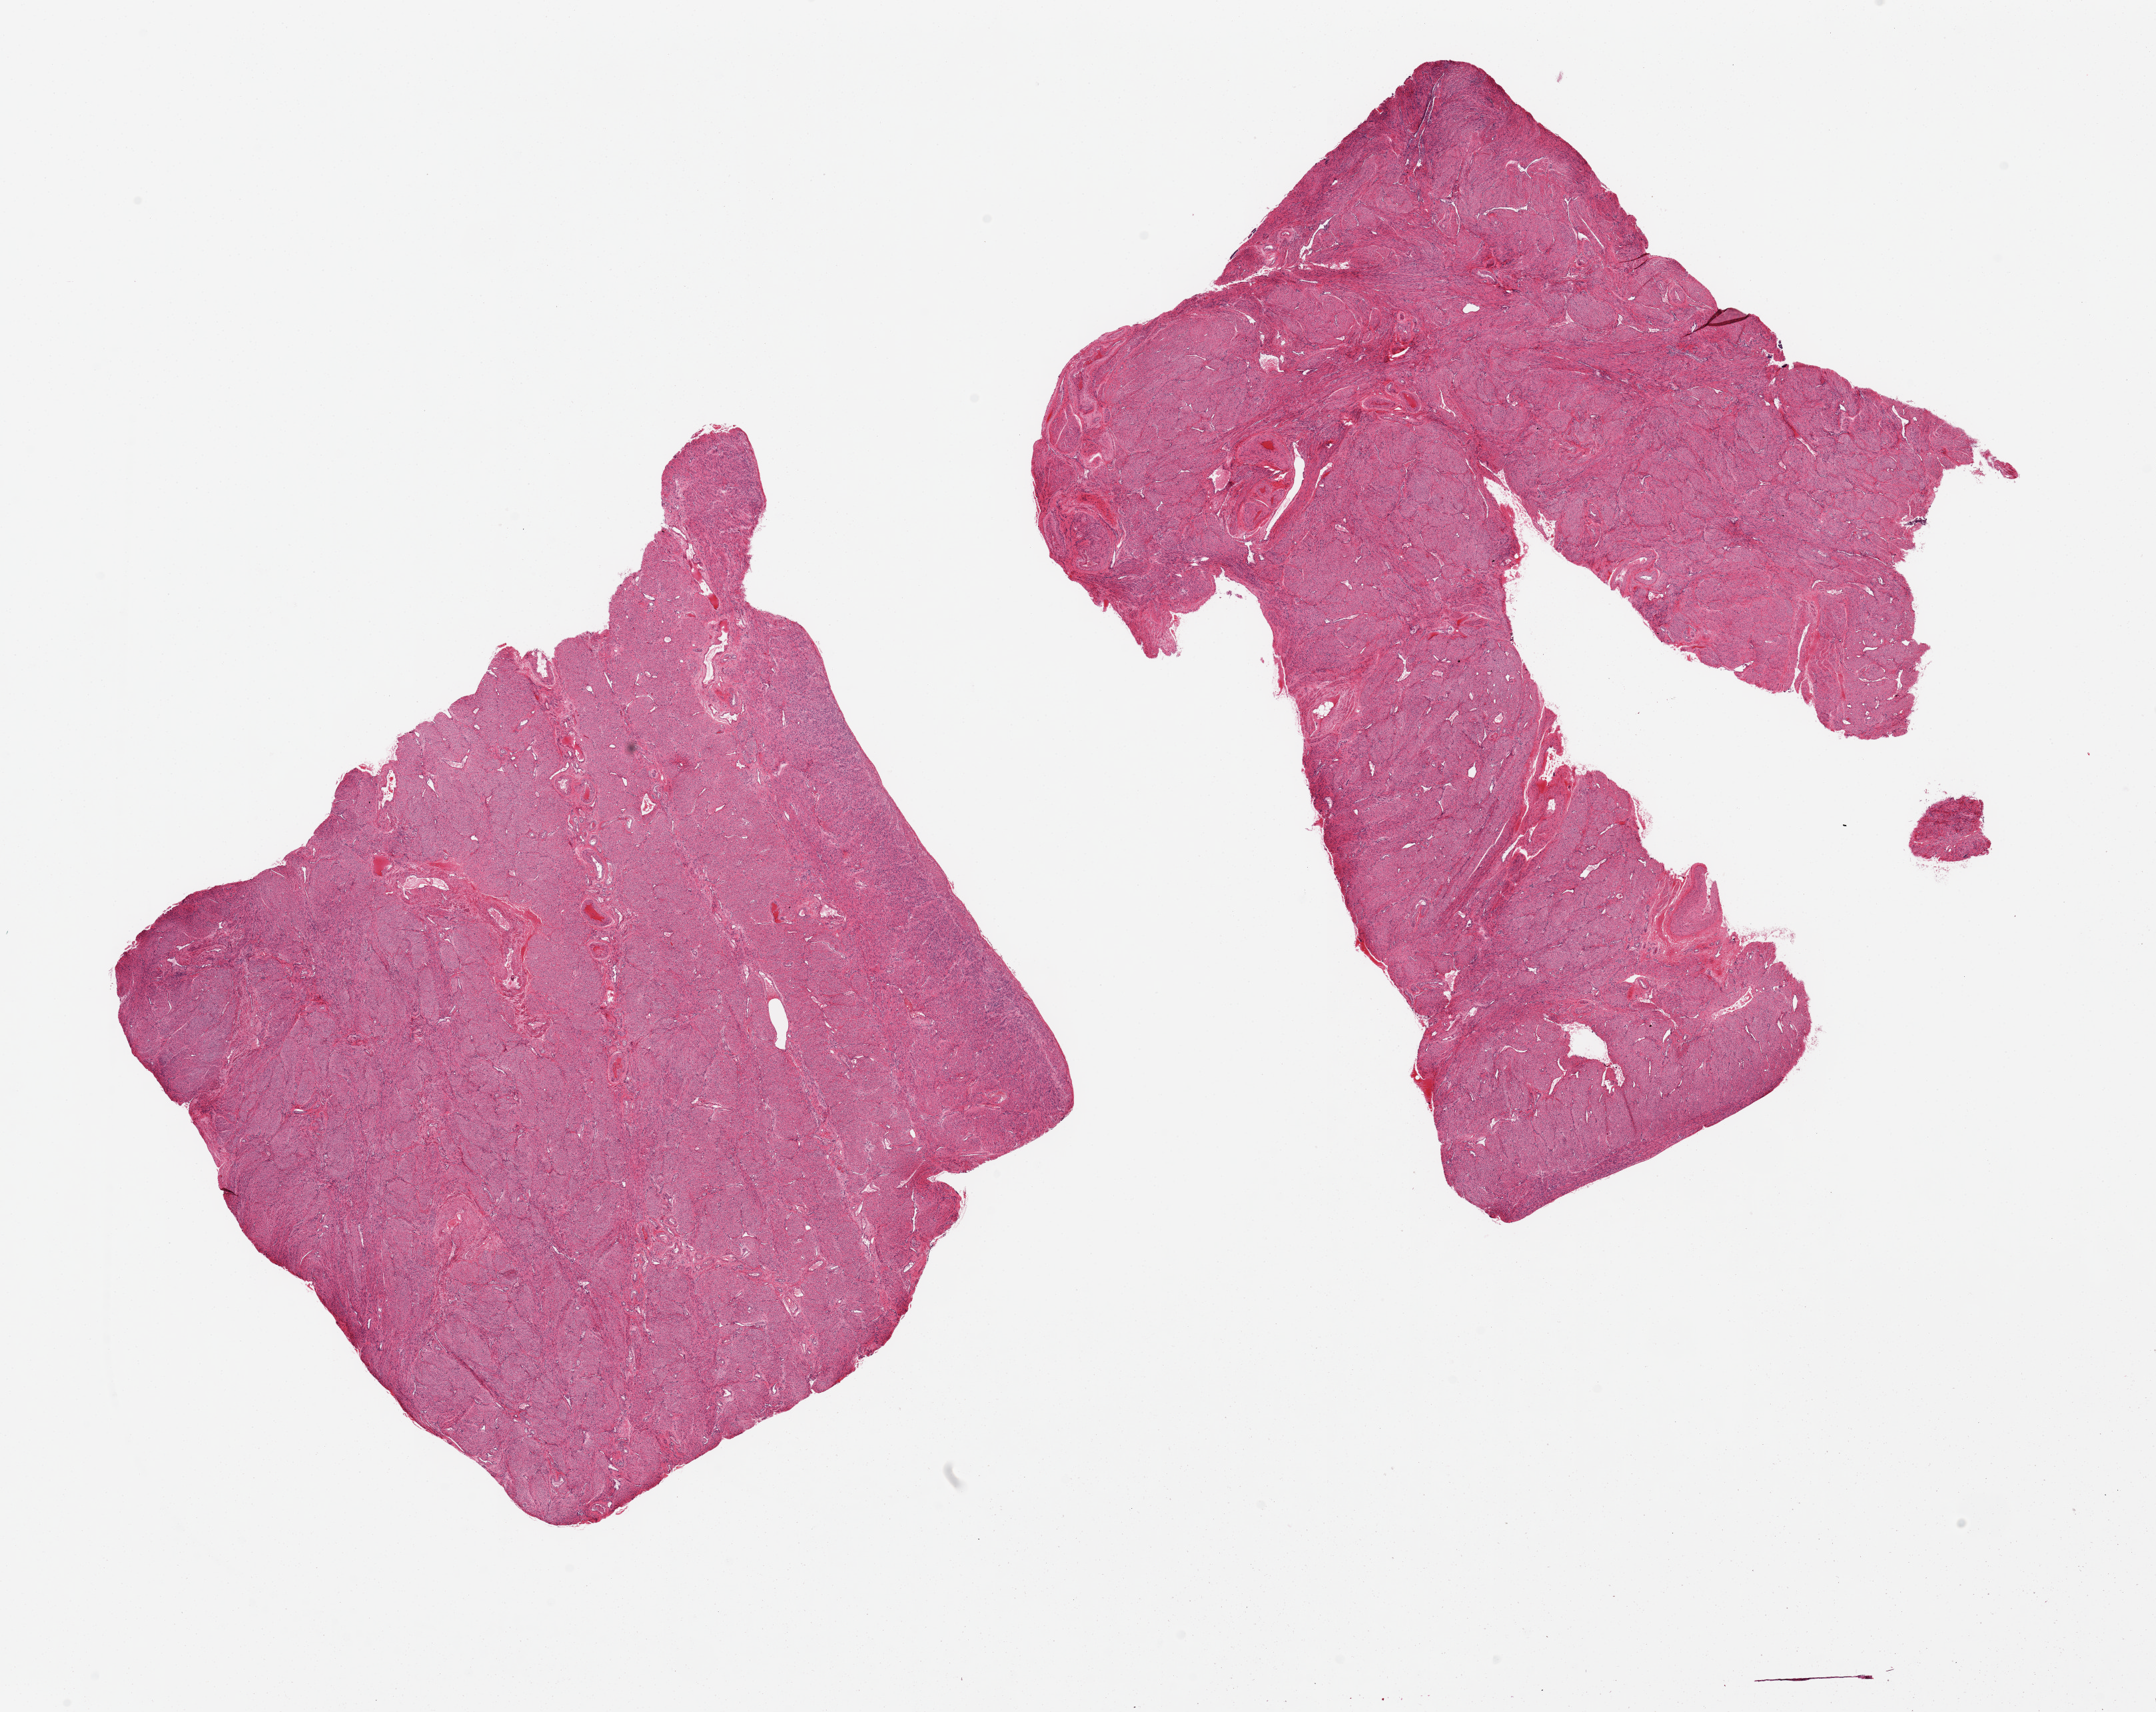
H&E whole-slide image, whole scanned area (about 25.6 x 20.3 mm) shown as a low-resolution overview, PAXgene-fixed, paraffin-embedded tissue, target tissue: uterus, donor tissue sample.
Review note (as recorded): 2 pieces, all myometrium, no endometrial/stromal tissue noted.